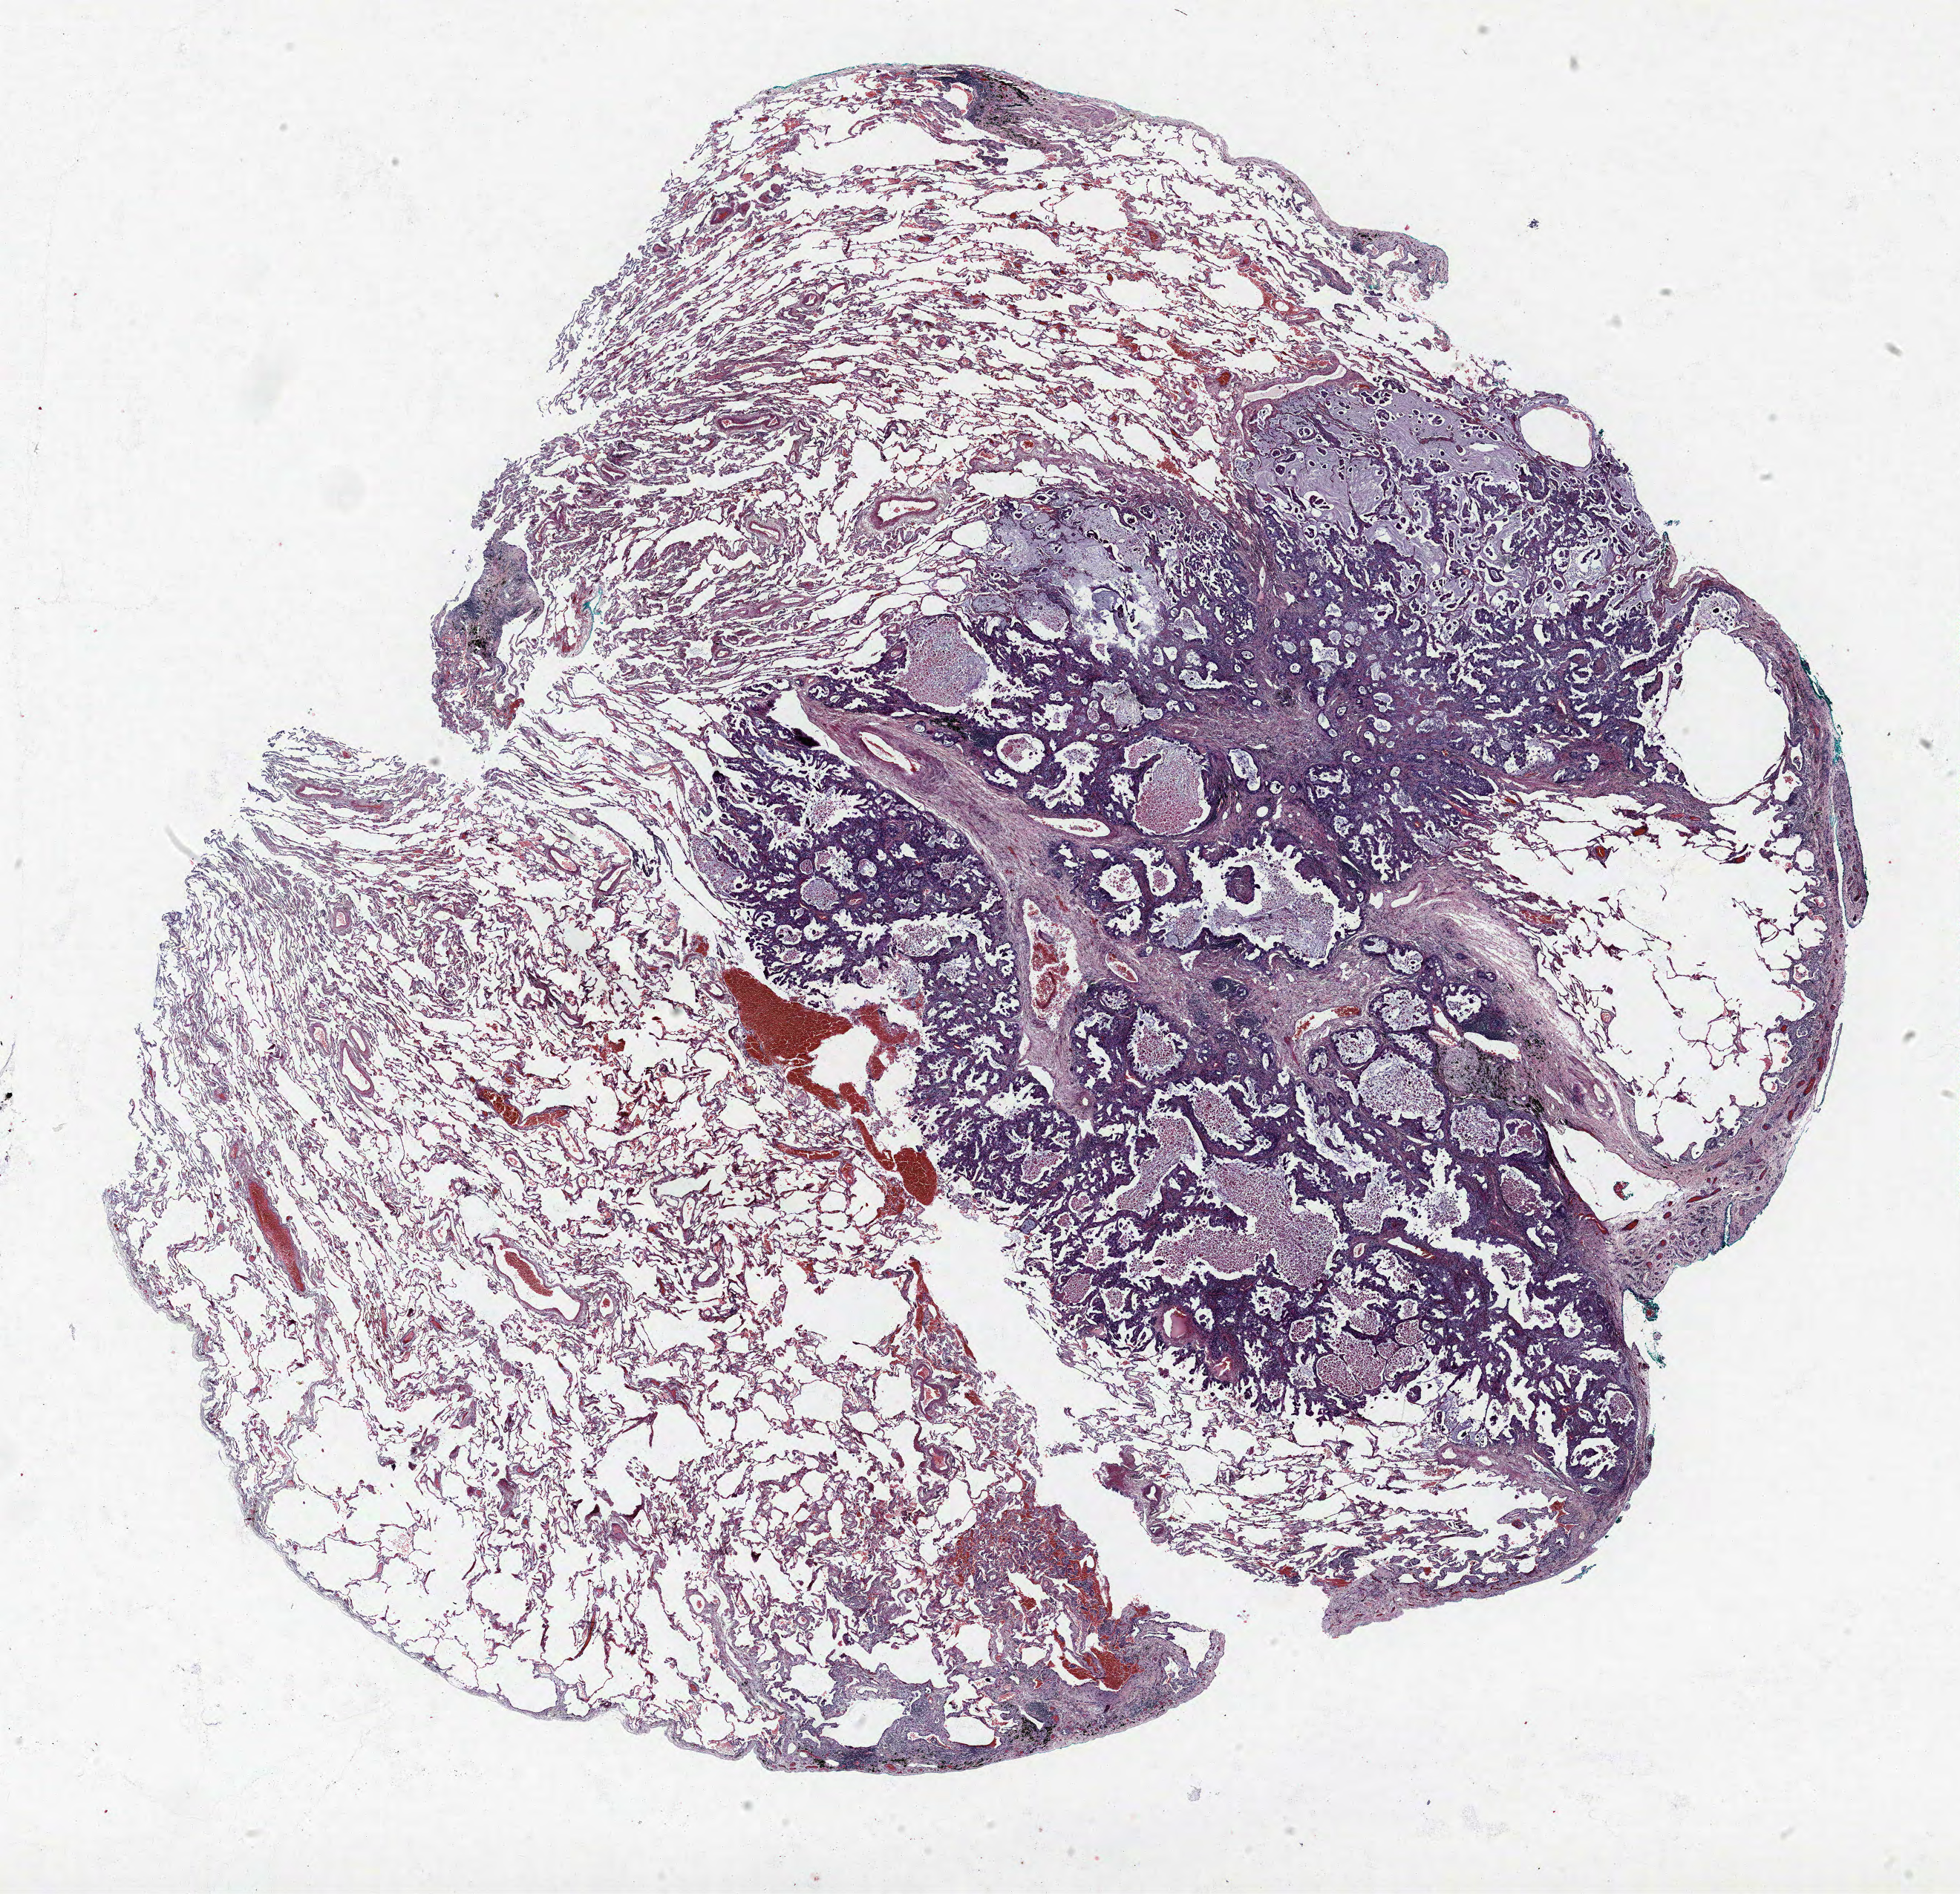
Hematoxylin and eosin (H&E) stained whole-slide image — low-resolution overview of the scanned area, about 21.1 x 20.4 mm (from a 40x scan); formalin-fixed paraffin-embedded (FFPE) section; lung. Male patient, aged 70 at enrolment. Former smoker at enrolment. Grade: moderately differentiated (G2).
Primary tumour location (clinical record): left upper lobe. ICD-O-3 topography: upper lobe of lung (C34.1). Tumour size (pathology): 20 mm. Stage (AJCC 6th edition): IA. Participant's lung-cancer diagnosis: Mucin-producing adenocarcinoma.